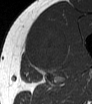
MRI of an extremity soft-tissue mass, one axial slice. Position 36 of 62 along the scan axis. MR volume resampled by the dataset authors to the PET/CT grid (not the native acquisition matrix). 3.27 mm slice thickness. 92 × 104 image matrix. Male patient. From the clinical record (not read from this slice): histological type: mixoid liposarcoma; grade: low; site of the primary tumour: left thigh.
Annotated regions visible in this slice (expert contour drawn on MRI and transferred to this co-registered scan by the dataset authors):
- gross tumour volume (mass): box from (x=25, y=26) to (x=68, y=71) px